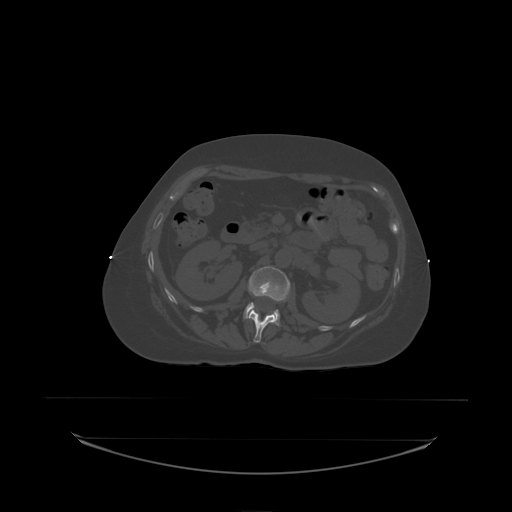
CT including the spine, one axial slice; bone window (W 1800 / L 400 HU); 512 × 512 image matrix. Patient: female, 53 years. Case-level facts recorded for this patient, not image findings: primary cancer: lung.
Annotated regions visible in this slice (semi-automatically segmented with operator editing):
- L1 vertebra: bounding box <249,309,275,338> (left, top, right, bottom; pixels)
- L2 vertebra: <244,267,291,327>